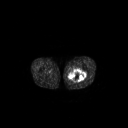
FDG PET of an extremity soft-tissue mass (from a PET/CT study), one axial slice. 3.27 mm slice thickness. 128 × 128 image matrix, field of view 700 × 700 mm. Patient: male, 44 years. Case-level facts recorded for this patient, not image findings: histological type: undifferentiated pleomorphic liposarcoma; grade: high; site of the primary tumour: left thigh.
Outlined on this slice (expert contour drawn on MRI and transferred to this co-registered scan by the dataset authors):
- gross tumour volume including surrounding oedema: bounding box <67,69,86,83> (left, top, right, bottom; pixels)
- gross tumour volume (mass): <68,69,86,81>